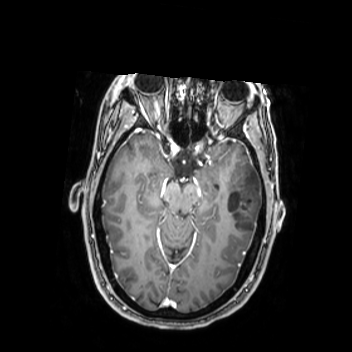
Brain MRI from a brain-tumour surgery series, one axial slice; position 161 of 350 along the scan axis; T1-weighted post-contrast; 0.9 mm slice thickness; 352 × 352 image matrix, field of view 280 × 280 mm. Case-level facts recorded for this patient, not image findings: histopathology: Oligodendroglioma; WHO grade: 2; IDH mutation: yes.
Annotated regions visible in this slice (manually delineated by an expert):
- tumour: box from (x=224, y=163) to (x=262, y=236) px